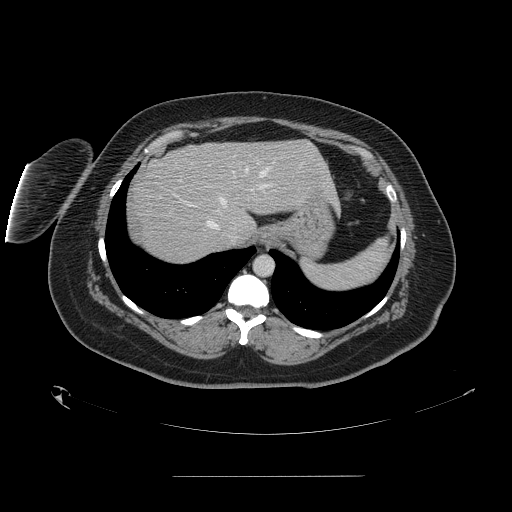
Contrast-enhanced abdominal CT, one axial slice. Position 124 of 164 along the scan axis. Intravenous contrast given. Soft-tissue window (W 400 / L 40 HU). 2.5 mm slice thickness. 512 × 512 image matrix, field of view 495 × 495 mm. Female patient, age 52 years. Case-level facts recorded for this patient, not image findings: diagnosis: colorectal cancer liver metastases, imaged before liver resection; multiple liver metastases: yes; largest metastasis: 3.5 cm; chemotherapy before resection: no.
Outlined on this slice (expert manual segmentation):
- hepatic veins: box from (x=206, y=167) to (x=269, y=239) px
- liver: (x=130, y=141)–(x=336, y=264)
- planned liver remnant (the part of the liver to remain after resection): (x=170, y=140)–(x=336, y=225)
- portal vein (with intrahepatic branches): (x=179, y=180)–(x=268, y=189)